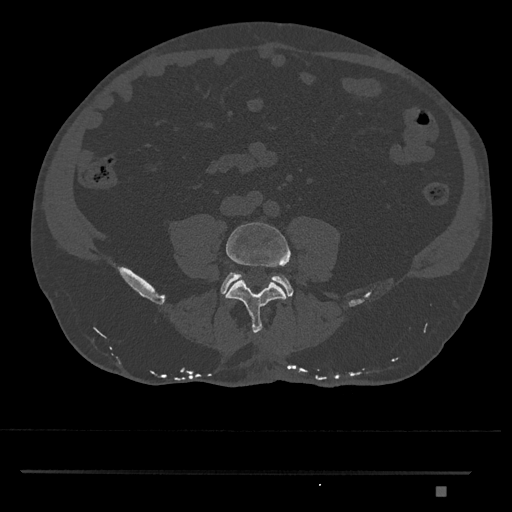
CT including the spine, one axial slice; slice 597 of 1134 in the series (ordered by position); reconstruction kernel Br40s/3; bone window (W 1800 / L 400 HU); 512 × 512 image matrix, field of view 429 × 429 mm. Patient: male, 65 years. Case-level facts recorded for this patient, not image findings: primary cancer: prostate.
Structures marked on this image (semi-automatic segmentation, software-assisted and operator-edited):
- L4 vertebra: box from (x=225, y=222) to (x=290, y=334) px
- L5 vertebra: (x=220, y=272)–(x=293, y=296)